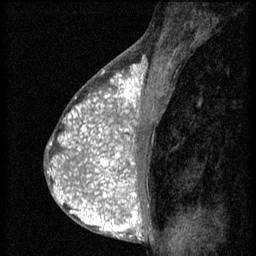
Breast MRI (dynamic contrast-enhanced), one sagittal slice. Position 32 of 60 along the scan axis. 3 images stored at this slice position (order not interpretable as contrast timing). 1.5 T. TE 4.2 ms, TR 8.2 ms. 2 mm slice thickness. 256 × 256 image matrix, field of view 180 × 180 mm. Patient: female, 38 years.
Annotated regions visible in this slice (semi-automatically segmented with operator editing):
- analysis volume of interest (the breast-tissue region the enhancement analysis was run in; not a lesion): bounding box (x1, y1, x2, y2) in pixels: (92, 112, 151, 171)
- tumour enhancement mask (voxels above the 70 % enhancement threshold inside the analysis volume of interest): (92, 112, 139, 171)